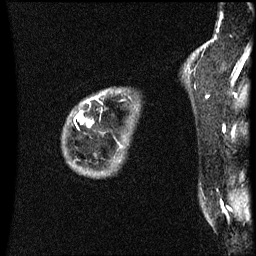
Breast MRI (dynamic contrast-enhanced), one sagittal slice. Position 48 of 60 along the scan axis. Dynamic contrast-enhanced series, image 2 of 3 at this slice position (ordered by acquisition). 1.5 T. TE 4.2 ms, TR 8.9 ms. 256 × 256 image matrix, field of view 200 × 200 mm. Patient: female, 44 years. Case-level facts recorded for this patient, not image findings: setting: breast cancer imaged before/during neoadjuvant chemotherapy; receptor status: HR-positive, HER2-negative.
Structures marked on this image (semi-automatic segmentation, software-assisted and operator-edited):
- analysis volume of interest (the breast-tissue region the enhancement analysis was run in; not a lesion): bounding box [x1, y1, x2, y2] px = [74, 94, 124, 147]
- tumour enhancement mask (voxels above the 70 % enhancement threshold inside the analysis volume of interest): [88, 122, 92, 125]